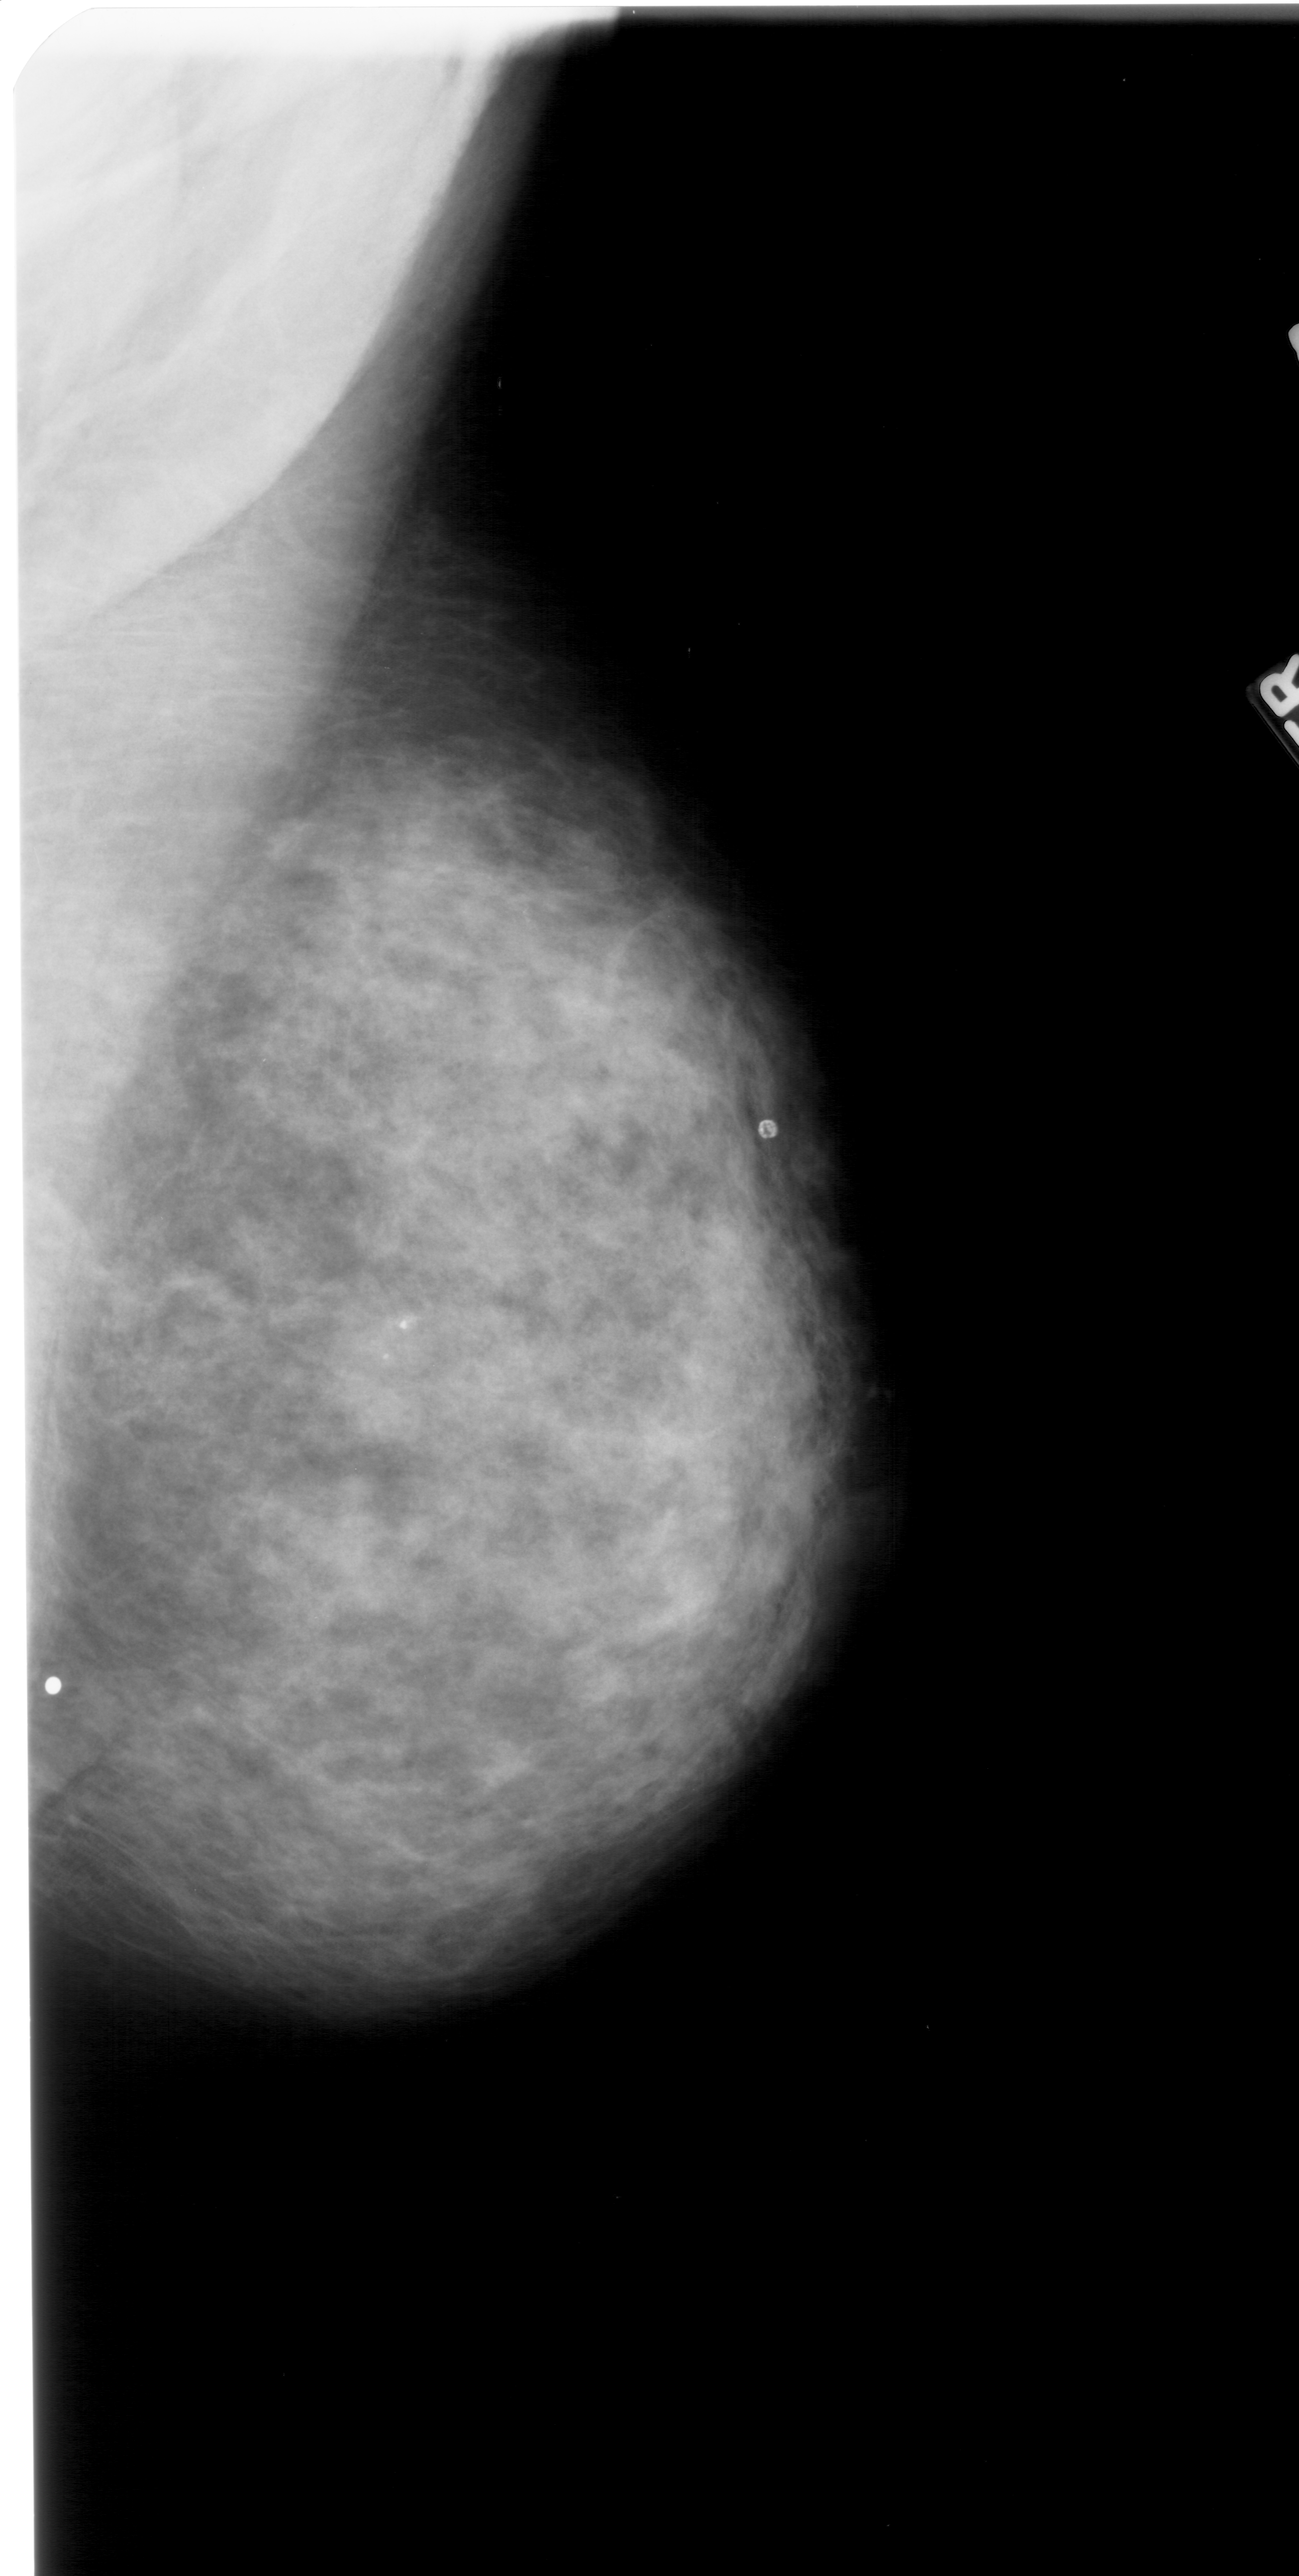
Mammogram (digitized film). Right breast. Mediolateral oblique (MLO) view. 1299 × 2576 image matrix.
Expert-marked regions of interest on this image (one box per marked abnormality):
- calcifications, morphology pleomorphic, distribution clustered; BI-RADS assessment category 4; subtlety rating 2 on a 1 (subtle) to 5 (obvious) scale; pathology (as recorded): malignant: bounding box (x1, y1, x2, y2) in pixels: (360, 1303, 437, 1385)